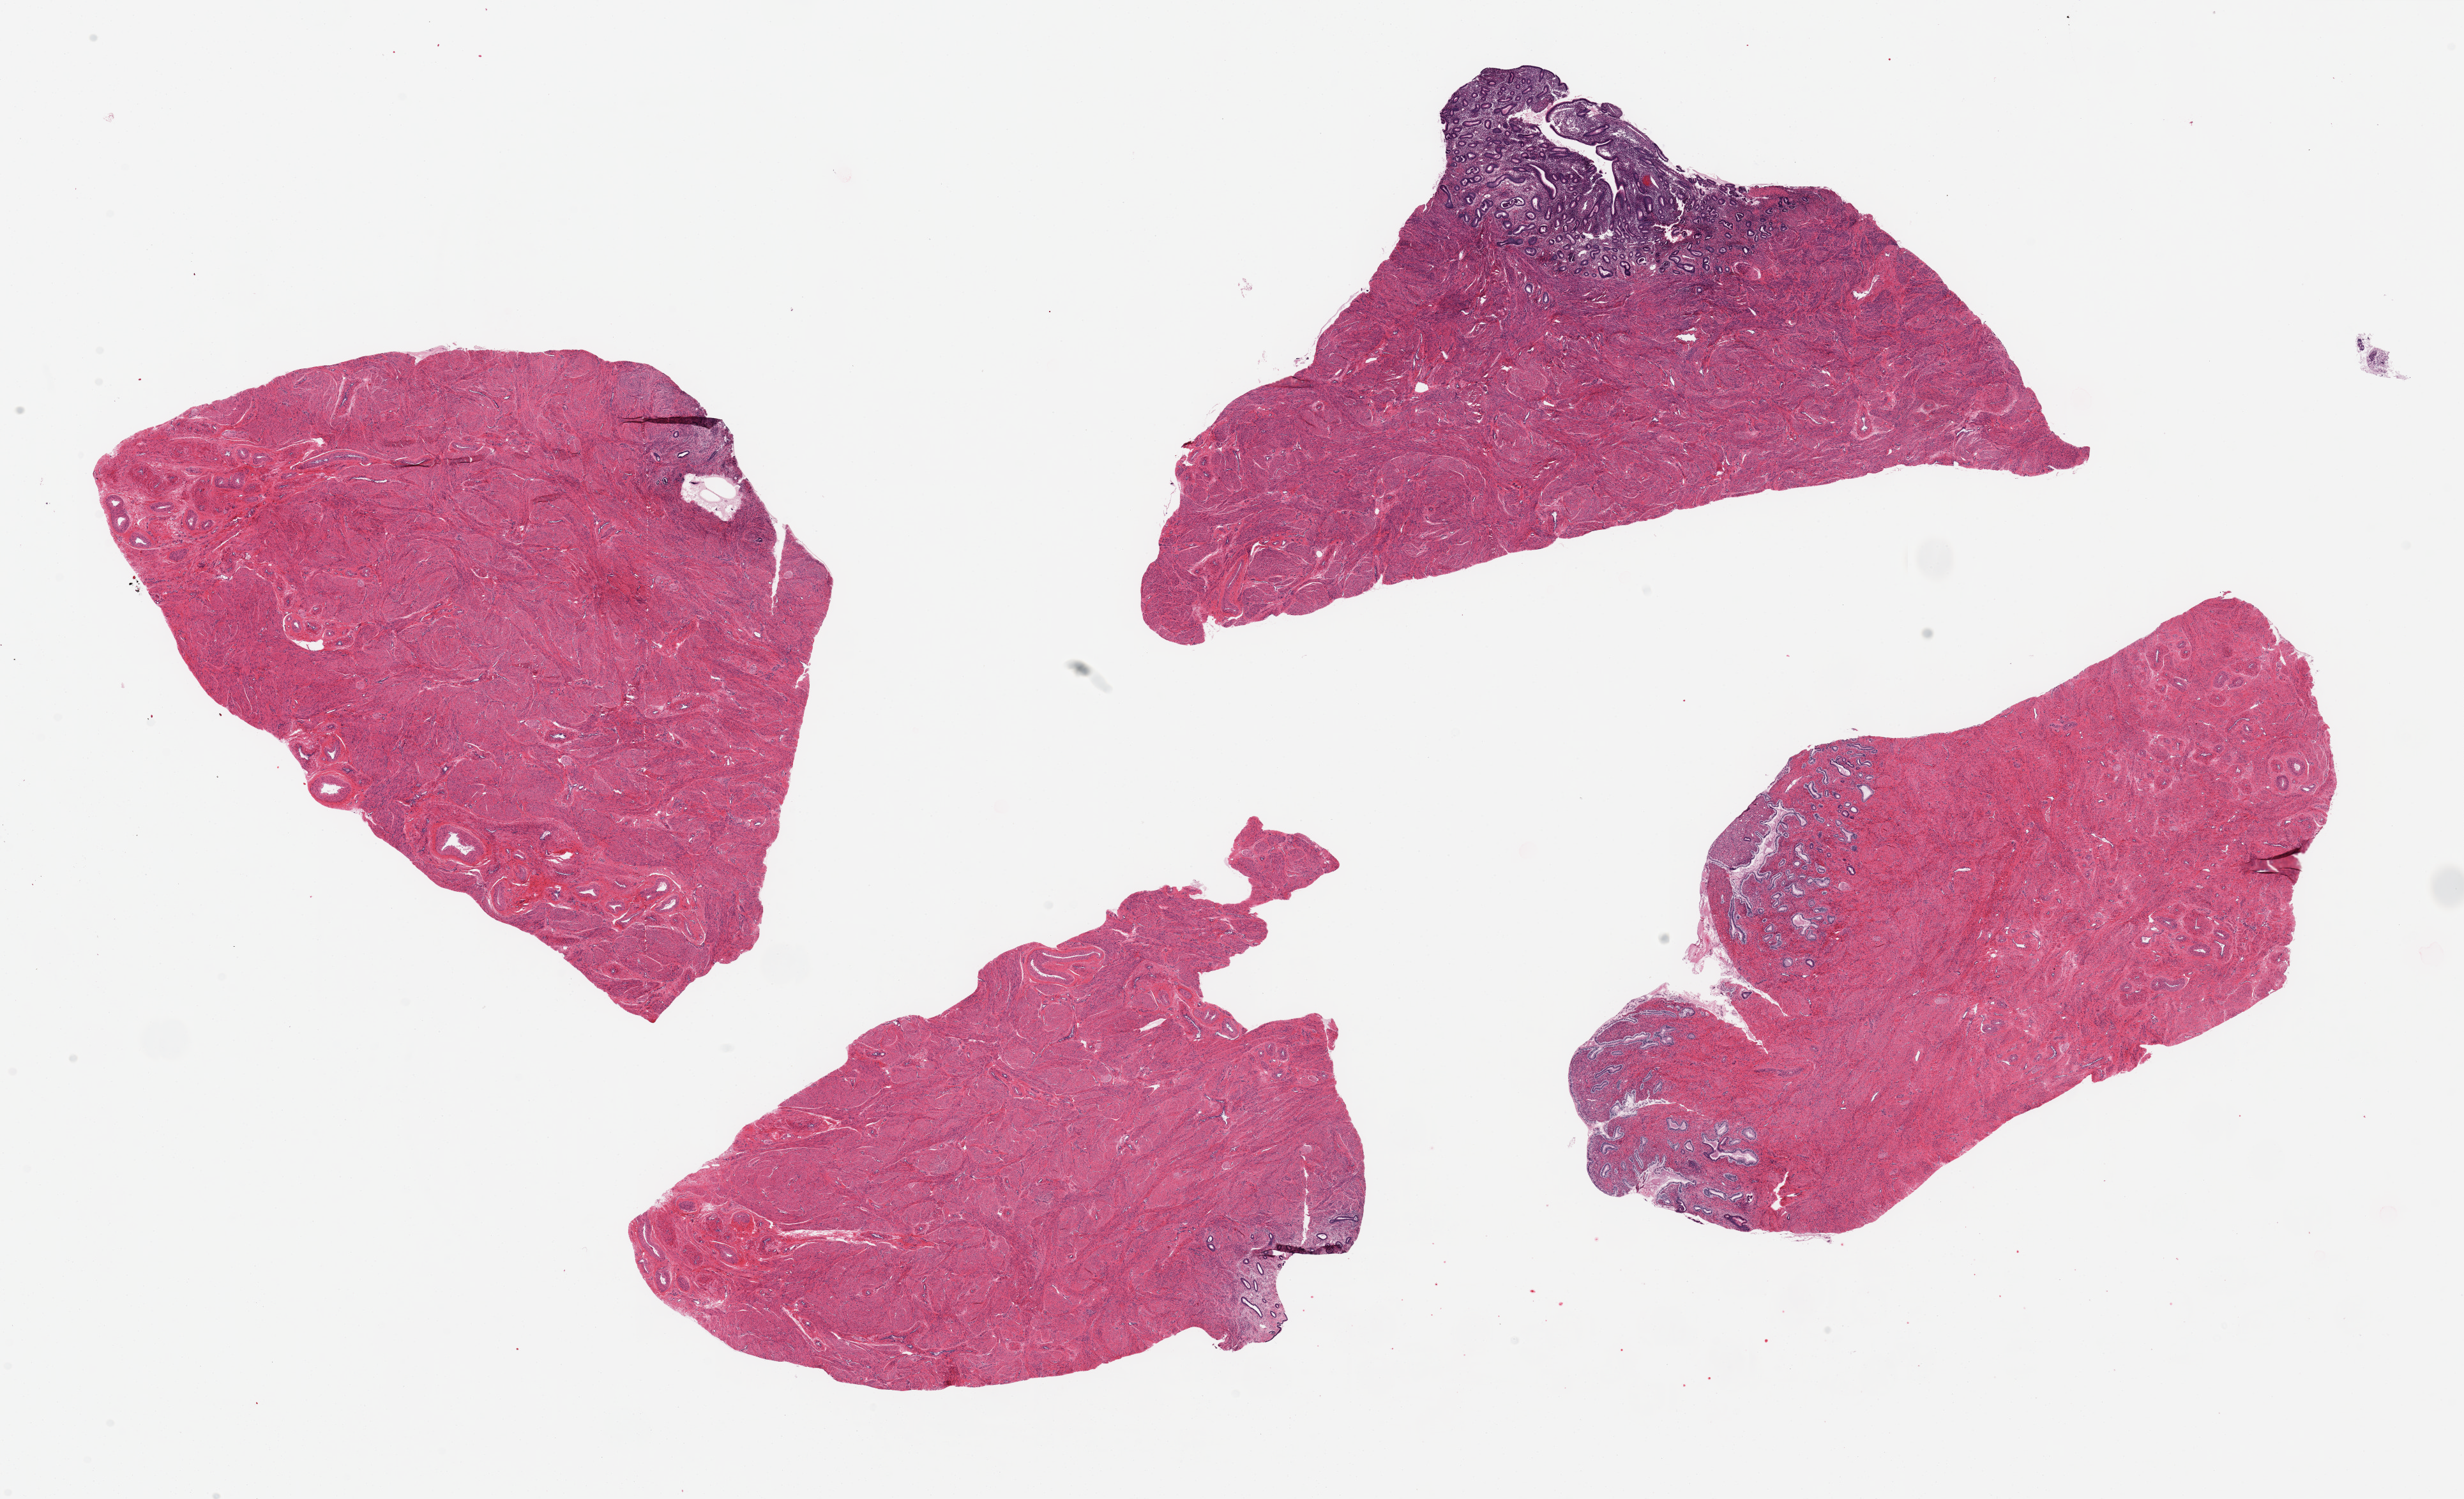
H&E whole-slide image — whole scanned area (about 30.5 x 18.6 mm) shown as a low-resolution overview; PAXgene-fixed, paraffin-embedded tissue; sampled site (target tissue): endocervix; tissue donor sample. Donor: female.
Pathologist's review note for this sample: 4 pieces, 2 are endocervix;2 are endometrium.